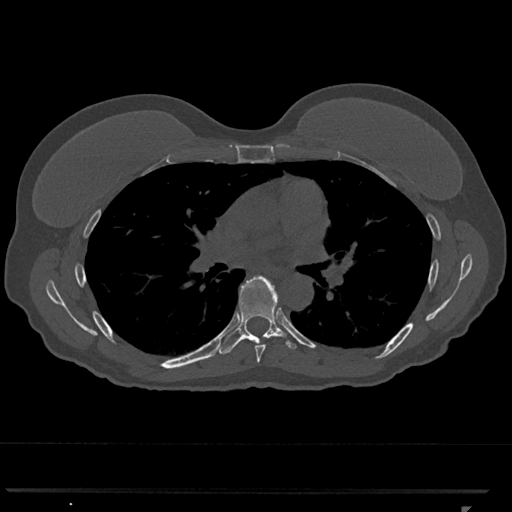
CT including the spine, one axial slice. Slice 732 of 793 in the series (ordered by position). 120 kVp. Bone window (W 1800 / L 400 HU). 0.5 mm slice thickness. 512 × 512 image matrix, field of view 380 × 380 mm. Patient: female, 62 years. From the clinical record (not read from this slice): primary cancer: renal.
Annotated regions visible in this slice (semi-automatic segmentation, software-assisted and operator-edited):
- T6 vertebra: bounding box (x1, y1, x2, y2) in pixels: (255, 342, 266, 363)
- T7 vertebra: (217, 276, 297, 354)